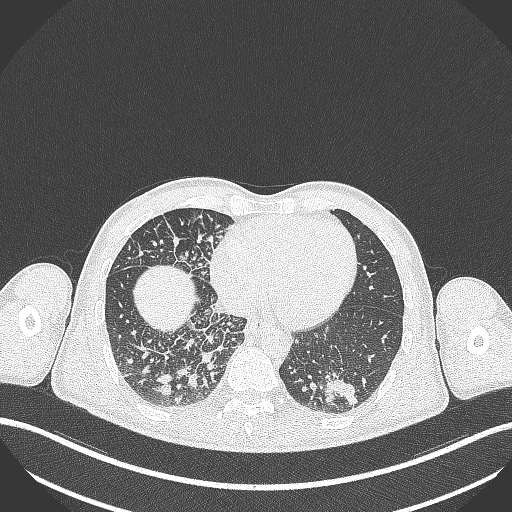
Chest CT, one axial slice. Reconstruction kernel B70f. Lung window (W 1500 / L -600 HU). 1 mm slice thickness. 512 × 512 image matrix, field of view 400 × 400 mm. Patient: male, 49 years. Case-level facts recorded for this patient, not image findings: clinical TNM (as recorded): T2b N1 M0.
Outlined on this slice (bounding box drawn by a radiologist):
- lung tumour (recorded histology: adenocarcinoma): bounding box (x1, y1, x2, y2) in pixels: (316, 368, 368, 412)